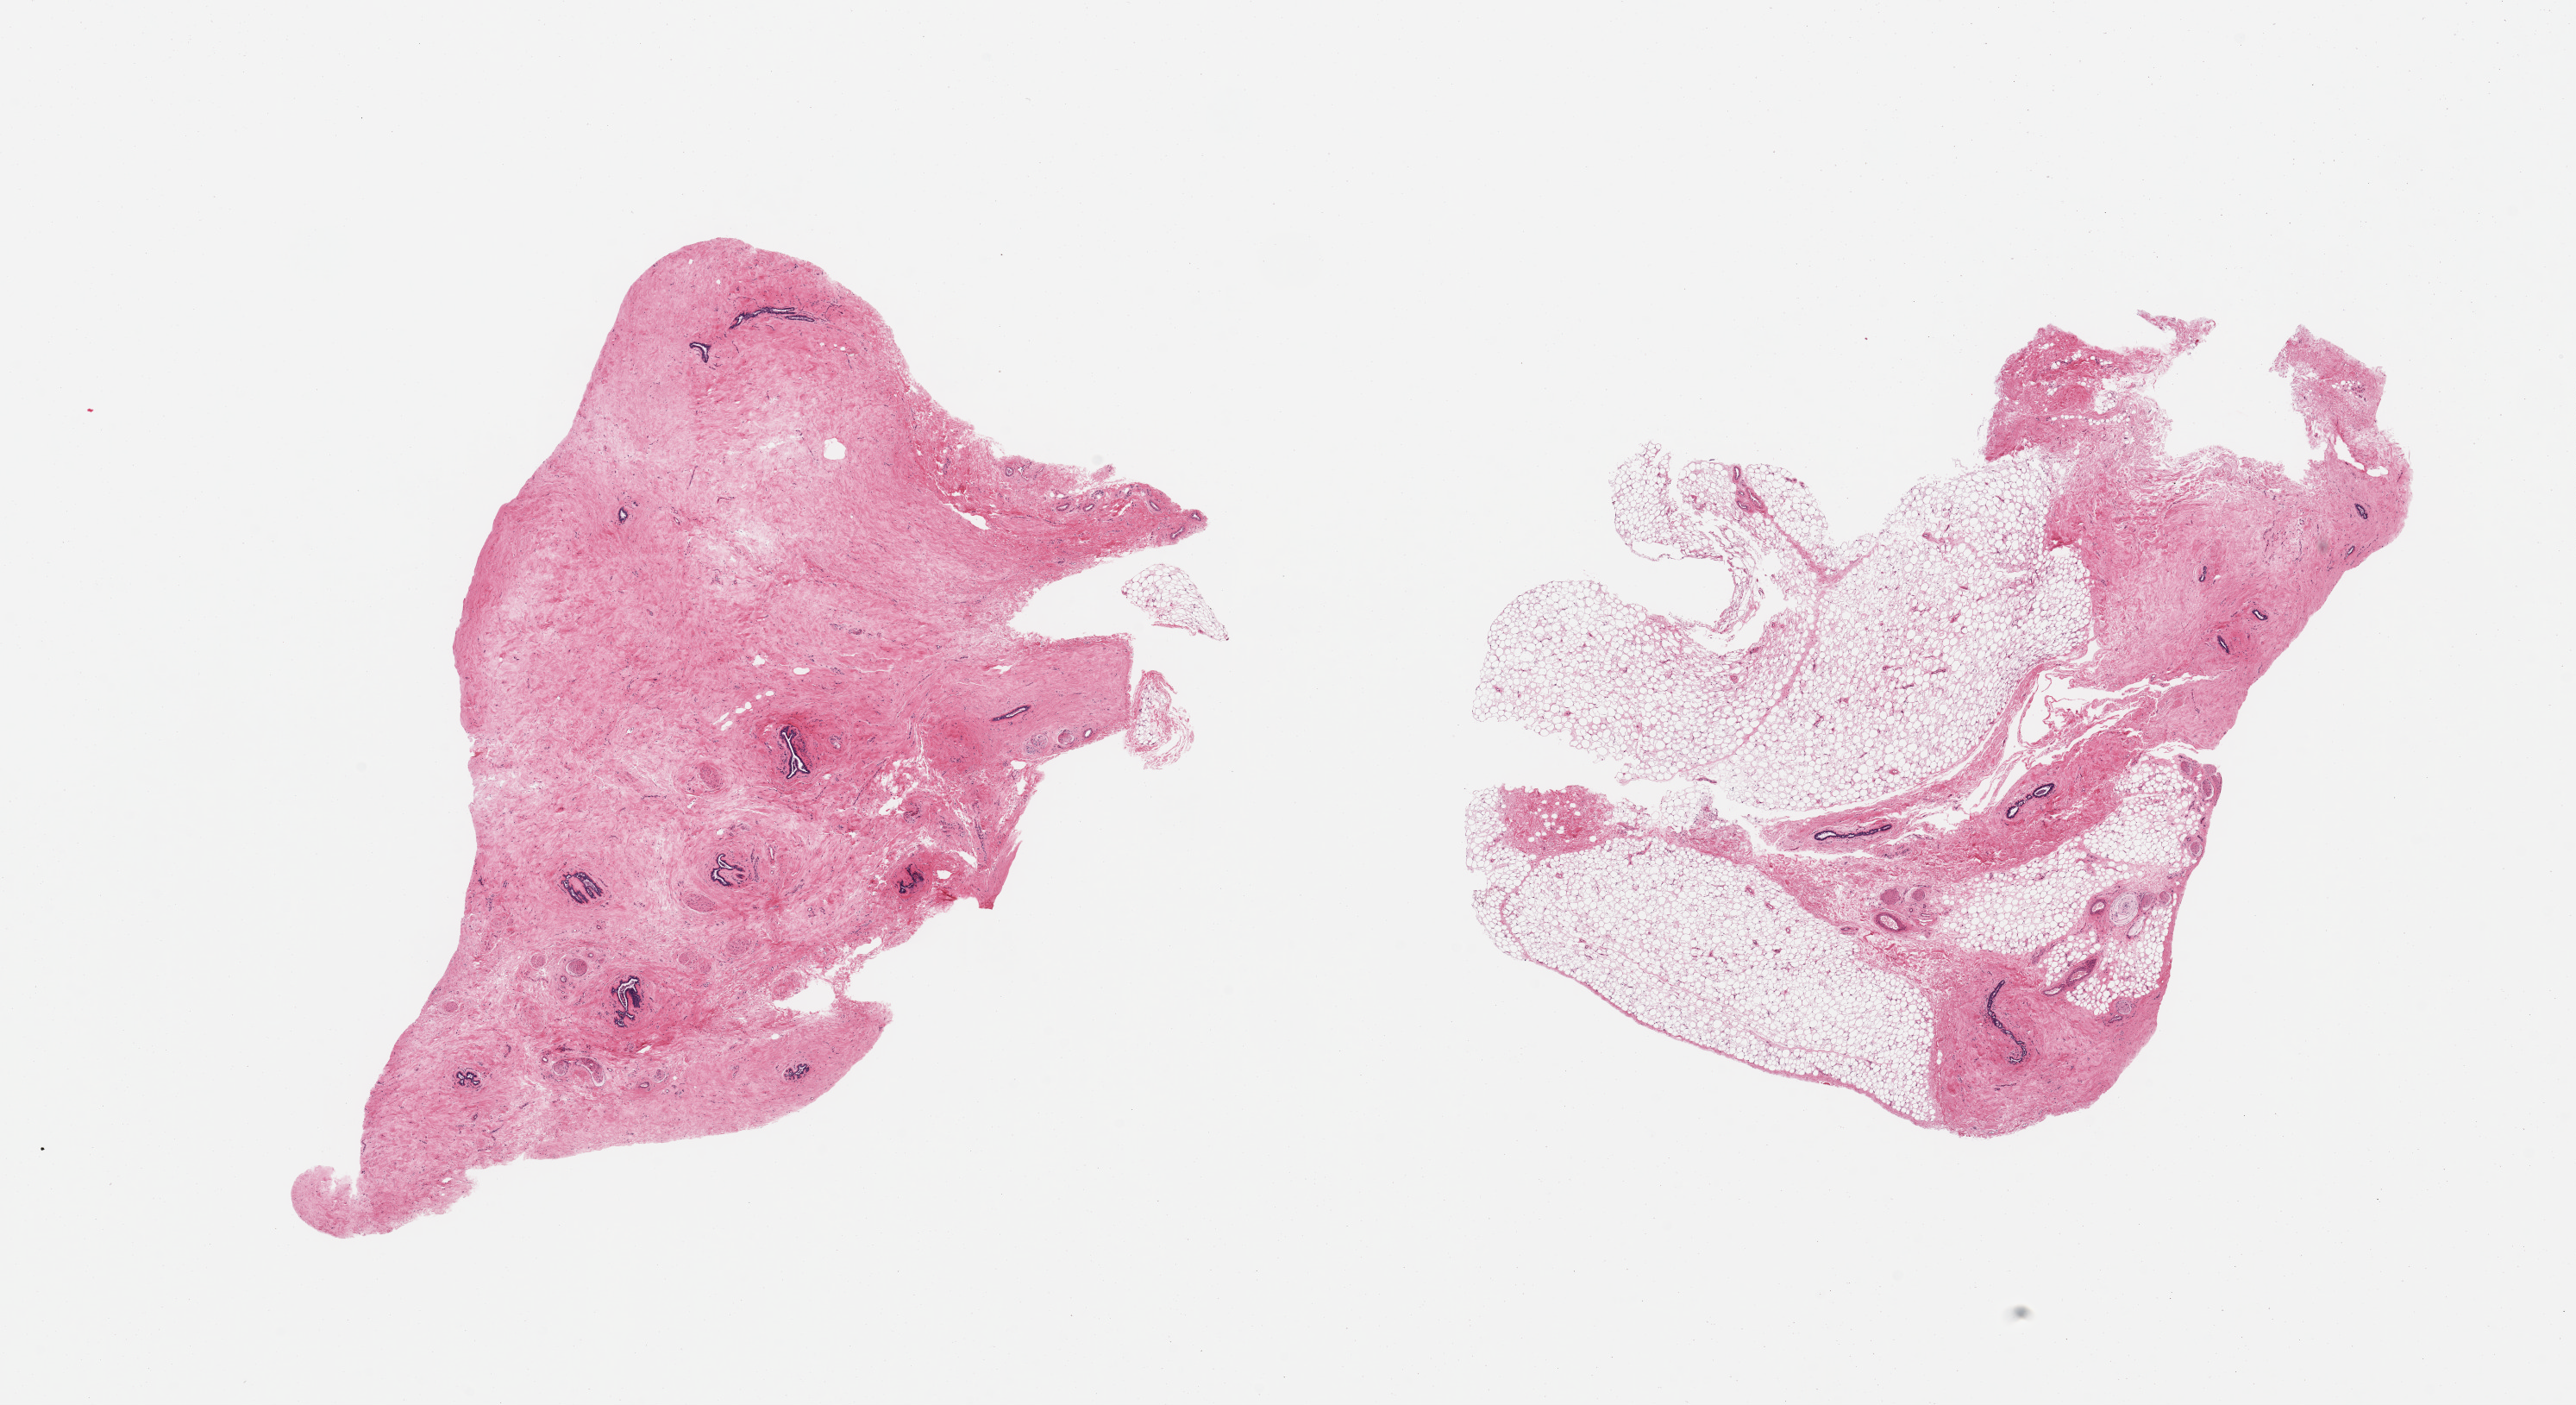
Hematoxylin and eosin (H&E) whole-slide image, brightfield, a low-resolution overview of the entire scanned area, about 23.6 x 12.9 mm (slide scanned at 20x), PAXgene-fixed paraffin-embedded (PFPE) section, sampled site (target tissue): breast, tissue donor sample. Donor sex: male.
- reviewer comment on this tissue sample: 2 pieces; one composed of fibrotic stroma and ductal structures and other composed of adipose tissue and fibrotic stroma with ductal structures suggestive of gynecomastoid stromal and glandular hyperplasia